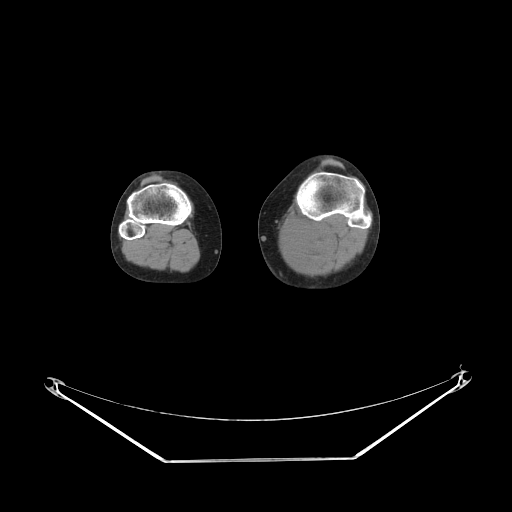
CT of an extremity soft-tissue mass (from a PET/CT study), one axial slice; position 159 of 223 along the scan axis; soft-tissue window (W 400 / L 40 HU); 3.75 mm slice thickness; 512 × 512 image matrix, field of view 500 × 500 mm. Female patient. Case-level facts recorded for this patient, not image findings: histological type: extraskeletal high grade osteogenic sarcoma; grade: high; site of the primary tumour: left calf.
Structures marked on this image (expert contour drawn on MRI and transferred to this co-registered scan by the dataset authors):
- gross tumour volume (mass): box from (x=281, y=226) to (x=334, y=268) px